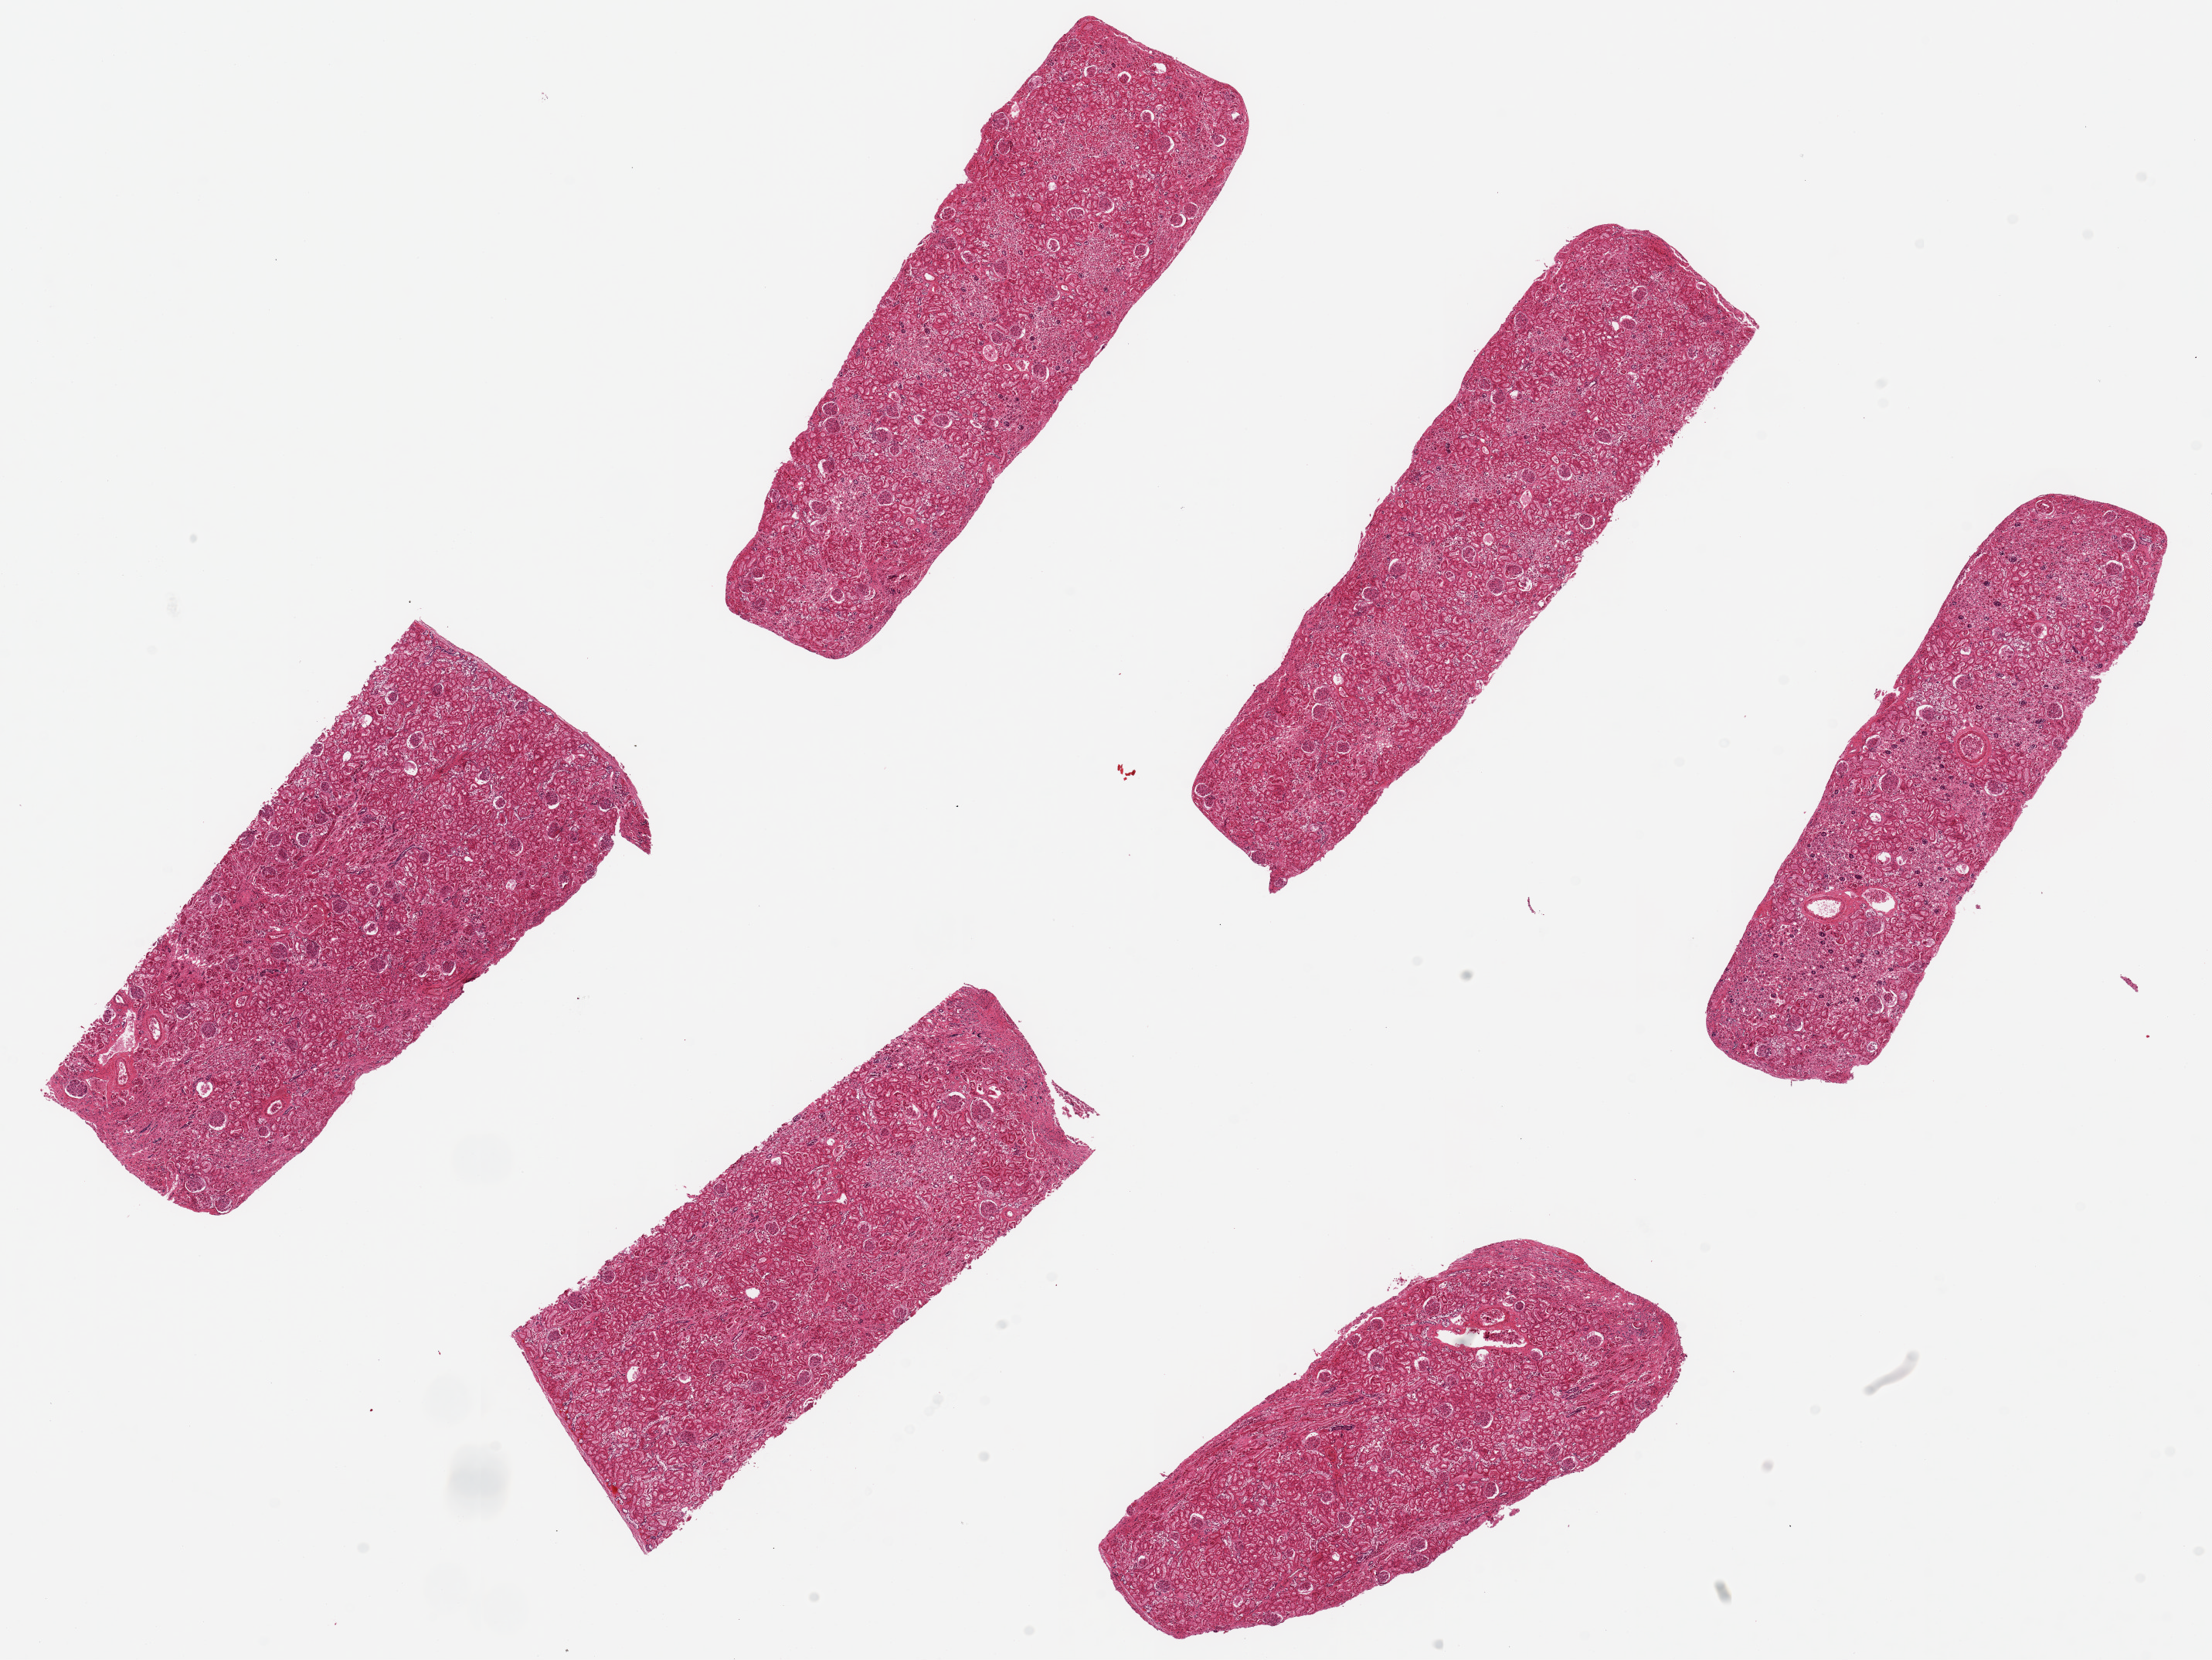
Hematoxylin and eosin (H&E) whole-slide image — shown as a low-resolution overview of the whole scanned area (about 22.6 x 17.0 mm). PAXgene-fixed paraffin-embedded (PFPE) section. Section of renal cortex (target tissue). Tissue donor sample. Male donor.
Reviewer comment on this tissue sample: 6 pieces 7x2.5mm, moderately autolyzed.